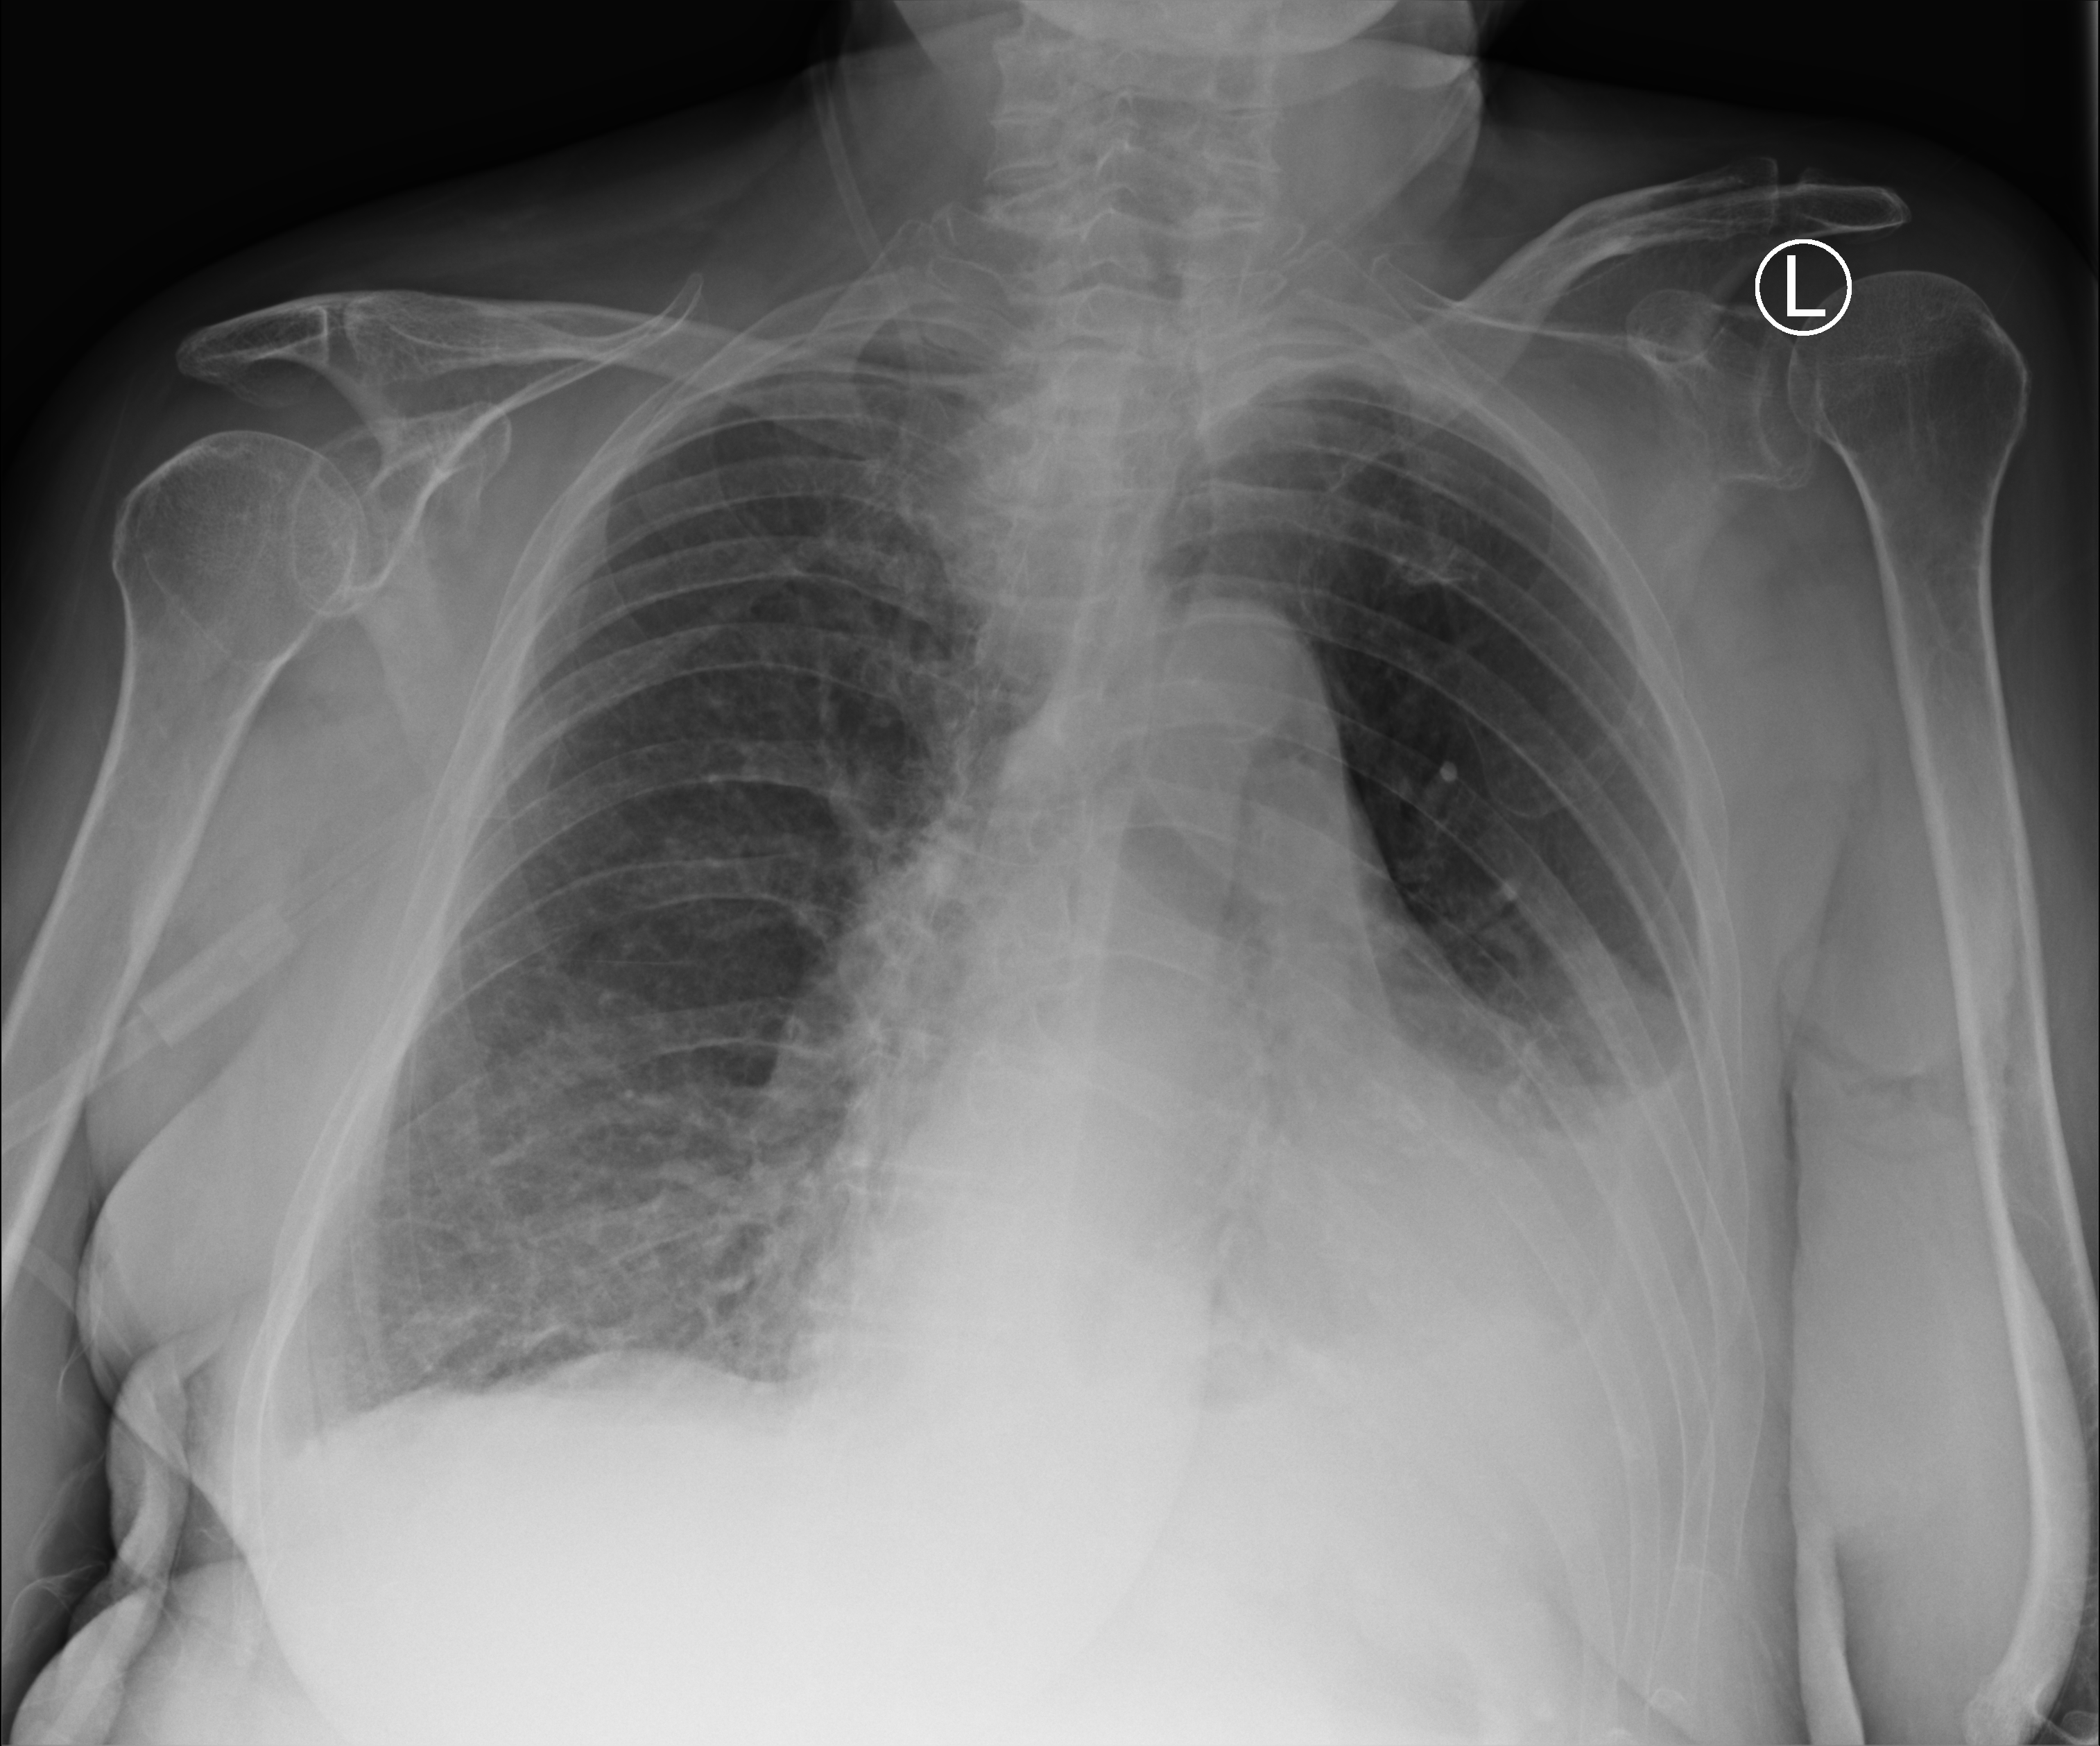
Chest X-ray (portable), anteroposterior (AP) projection. Female patient hospitalised with COVID-19, age 75–90 years.
From the hospital-stay record, not from the radiograph (when in the stay this image was taken is not recorded):
- mechanically ventilated during this hospital stay: no